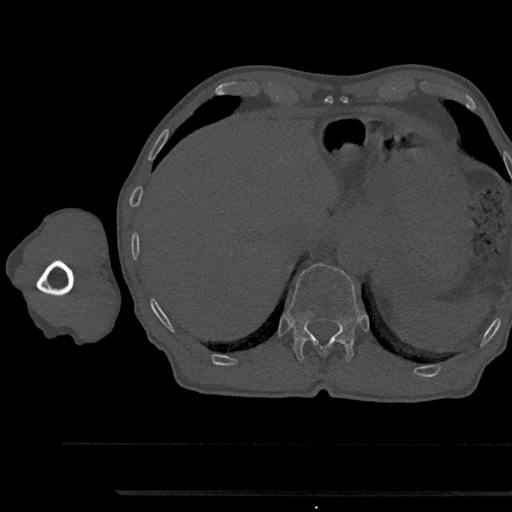
CT including the spine, one axial slice. Reconstruction kernel Br40s/3. 120 kVp. Bone window (W 1800 / L 400 HU). 512 × 512 image matrix, field of view 367 × 367 mm. Patient: male, 79 years. Case-level facts recorded for this patient, not image findings: primary cancer: prostate.
Outlined on this slice (semi-automatically segmented with operator editing):
- T12 vertebra: box from (x=287, y=263) to (x=360, y=362) px